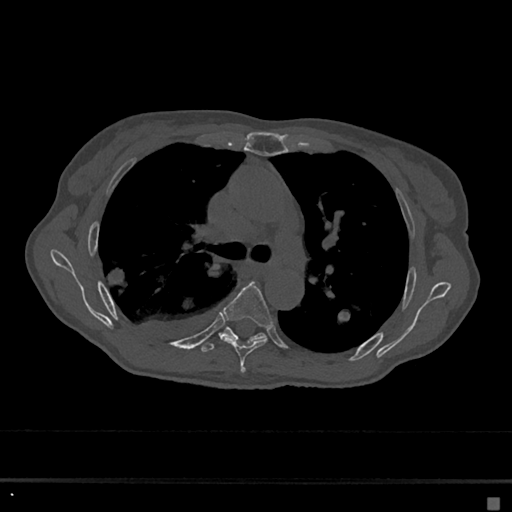
CT including the spine, one axial slice. Slice 448 of 797 in the series (ordered by position). Bone window (W 1800 / L 400 HU). 0.5 mm slice thickness. 512 × 512 image matrix. Patient: female, 68 years. Case-level facts recorded for this patient, not image findings: primary cancer: renal.
Outlined on this slice (semi-automatically segmented with operator editing):
- T5 vertebra: bounding box (x1, y1, x2, y2) in pixels: (223, 281, 273, 373)
- T6 vertebra: (201, 327, 266, 353)